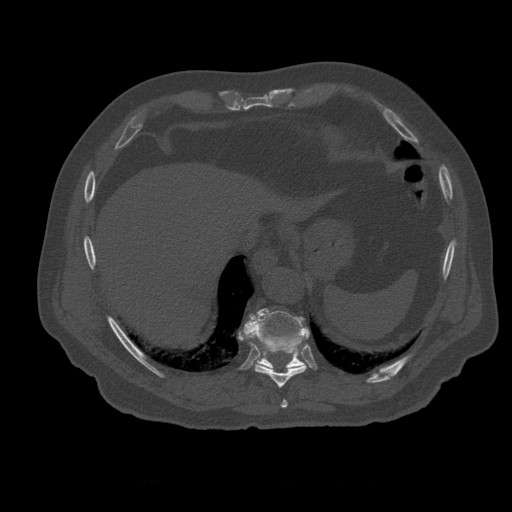
CT including the spine, one axial slice. Slice 313 of 399 in the series (ordered by position). Reconstruction kernel STANDARD. 120 kVp. Bone window (W 1800 / L 400 HU). 1.25 mm slice thickness. 512 × 512 image matrix. Patient age 73 years. Case-level facts recorded for this patient, not image findings: primary cancer: prostate.
Outlined on this slice (semi-automatic segmentation, software-assisted and operator-edited):
- T10 vertebra: bounding box [x1, y1, x2, y2] px = [240, 308, 310, 369]
- T12 vertebra: [267, 347, 280, 359]
- T8 vertebra: [281, 400, 288, 408]
- T9 vertebra: [240, 331, 307, 388]